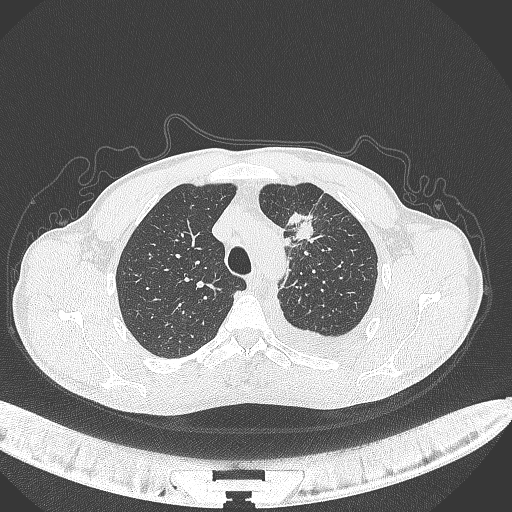
Chest CT, one axial slice; position 266 of 371 along the scan axis; reconstruction kernel B70f; 120 kVp; lung window (W 1500 / L -600 HU); 512 × 512 image matrix. Male patient, age 49 years. Case-level facts recorded for this patient, not image findings: clinical TNM (as recorded): T1c N1 M1.
Structures marked on this image (rectangle marked by the reading radiologist):
- lung tumour (recorded histology: adenocarcinoma): bounding box (x1, y1, x2, y2) in pixels: (282, 211, 321, 244)